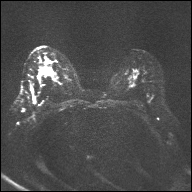
Breast MRI, one axial slice; position 18 of 32 along the scan axis; diffusion-weighted series; image 2 of 4 stored at this slice position (different b-values; order by instance number); 1.5 T; 4 mm slice thickness; 192 × 192 image matrix, field of view 360 × 360 mm. Female patient.
Structures marked on this image (outlined manually by an expert reader):
- tumour on diffusion-weighted imaging: bounding box (x1, y1, x2, y2) in pixels: (41, 67, 51, 73)